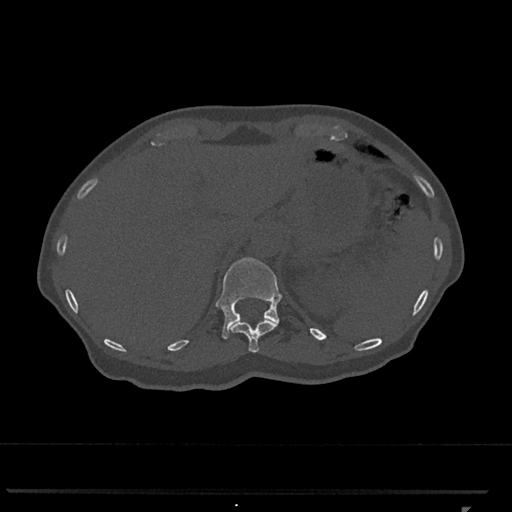
CT including the spine, one axial slice. Position 488 of 793 along the scan axis. Reconstruction kernel Br40s/3. 120 kVp. Bone window (W 1800 / L 400 HU). 0.5 mm slice thickness. 512 × 512 image matrix, field of view 380 × 380 mm. Patient: female, 62 years. Case-level facts recorded for this patient, not image findings: primary cancer: renal.
Outlined on this slice (semi-automatically segmented with operator editing):
- T11 vertebra: bounding box <230,319,278,353> (left, top, right, bottom; pixels)
- T12 vertebra: <215,257,283,339>